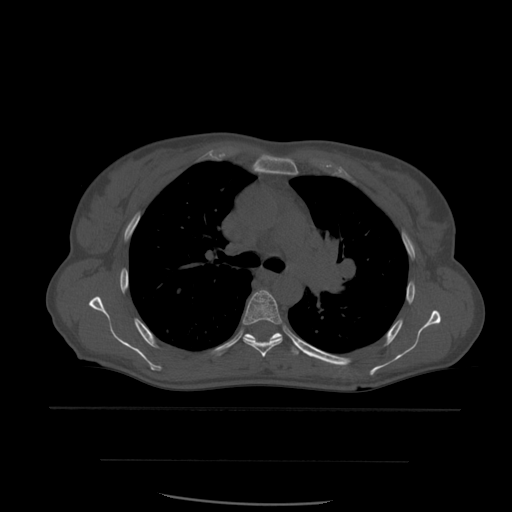
CT including the spine, one axial slice; slice 406 of 574 in the series (ordered by position); bone window (W 1800 / L 400 HU); 1.25 mm slice thickness; 512 × 512 image matrix. Patient age 48 years. From the clinical record (not read from this slice): primary cancer: lung; vertebrae with lytic lesions (as recorded): T11.
Outlined on this slice (semi-automatic segmentation, software-assisted and operator-edited):
- T5 vertebra: bounding box (x1, y1, x2, y2) in pixels: (243, 290, 283, 358)
- T6 vertebra: (244, 333, 300, 355)